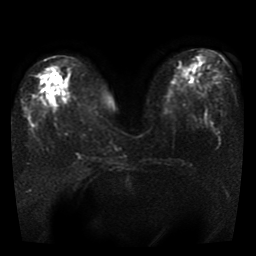
Breast MRI, one axial slice. Position 12 of 41 along the scan axis. Diffusion-weighted series; image 2 of 4 stored at this slice position (different b-values; order by instance number). 1.5 T. 256 × 256 image matrix, field of view 330 × 330 mm. Female patient.
Annotated regions visible in this slice (expert manual segmentation):
- tumour on diffusion-weighted imaging: bounding box (x1, y1, x2, y2) in pixels: (46, 93, 54, 103)